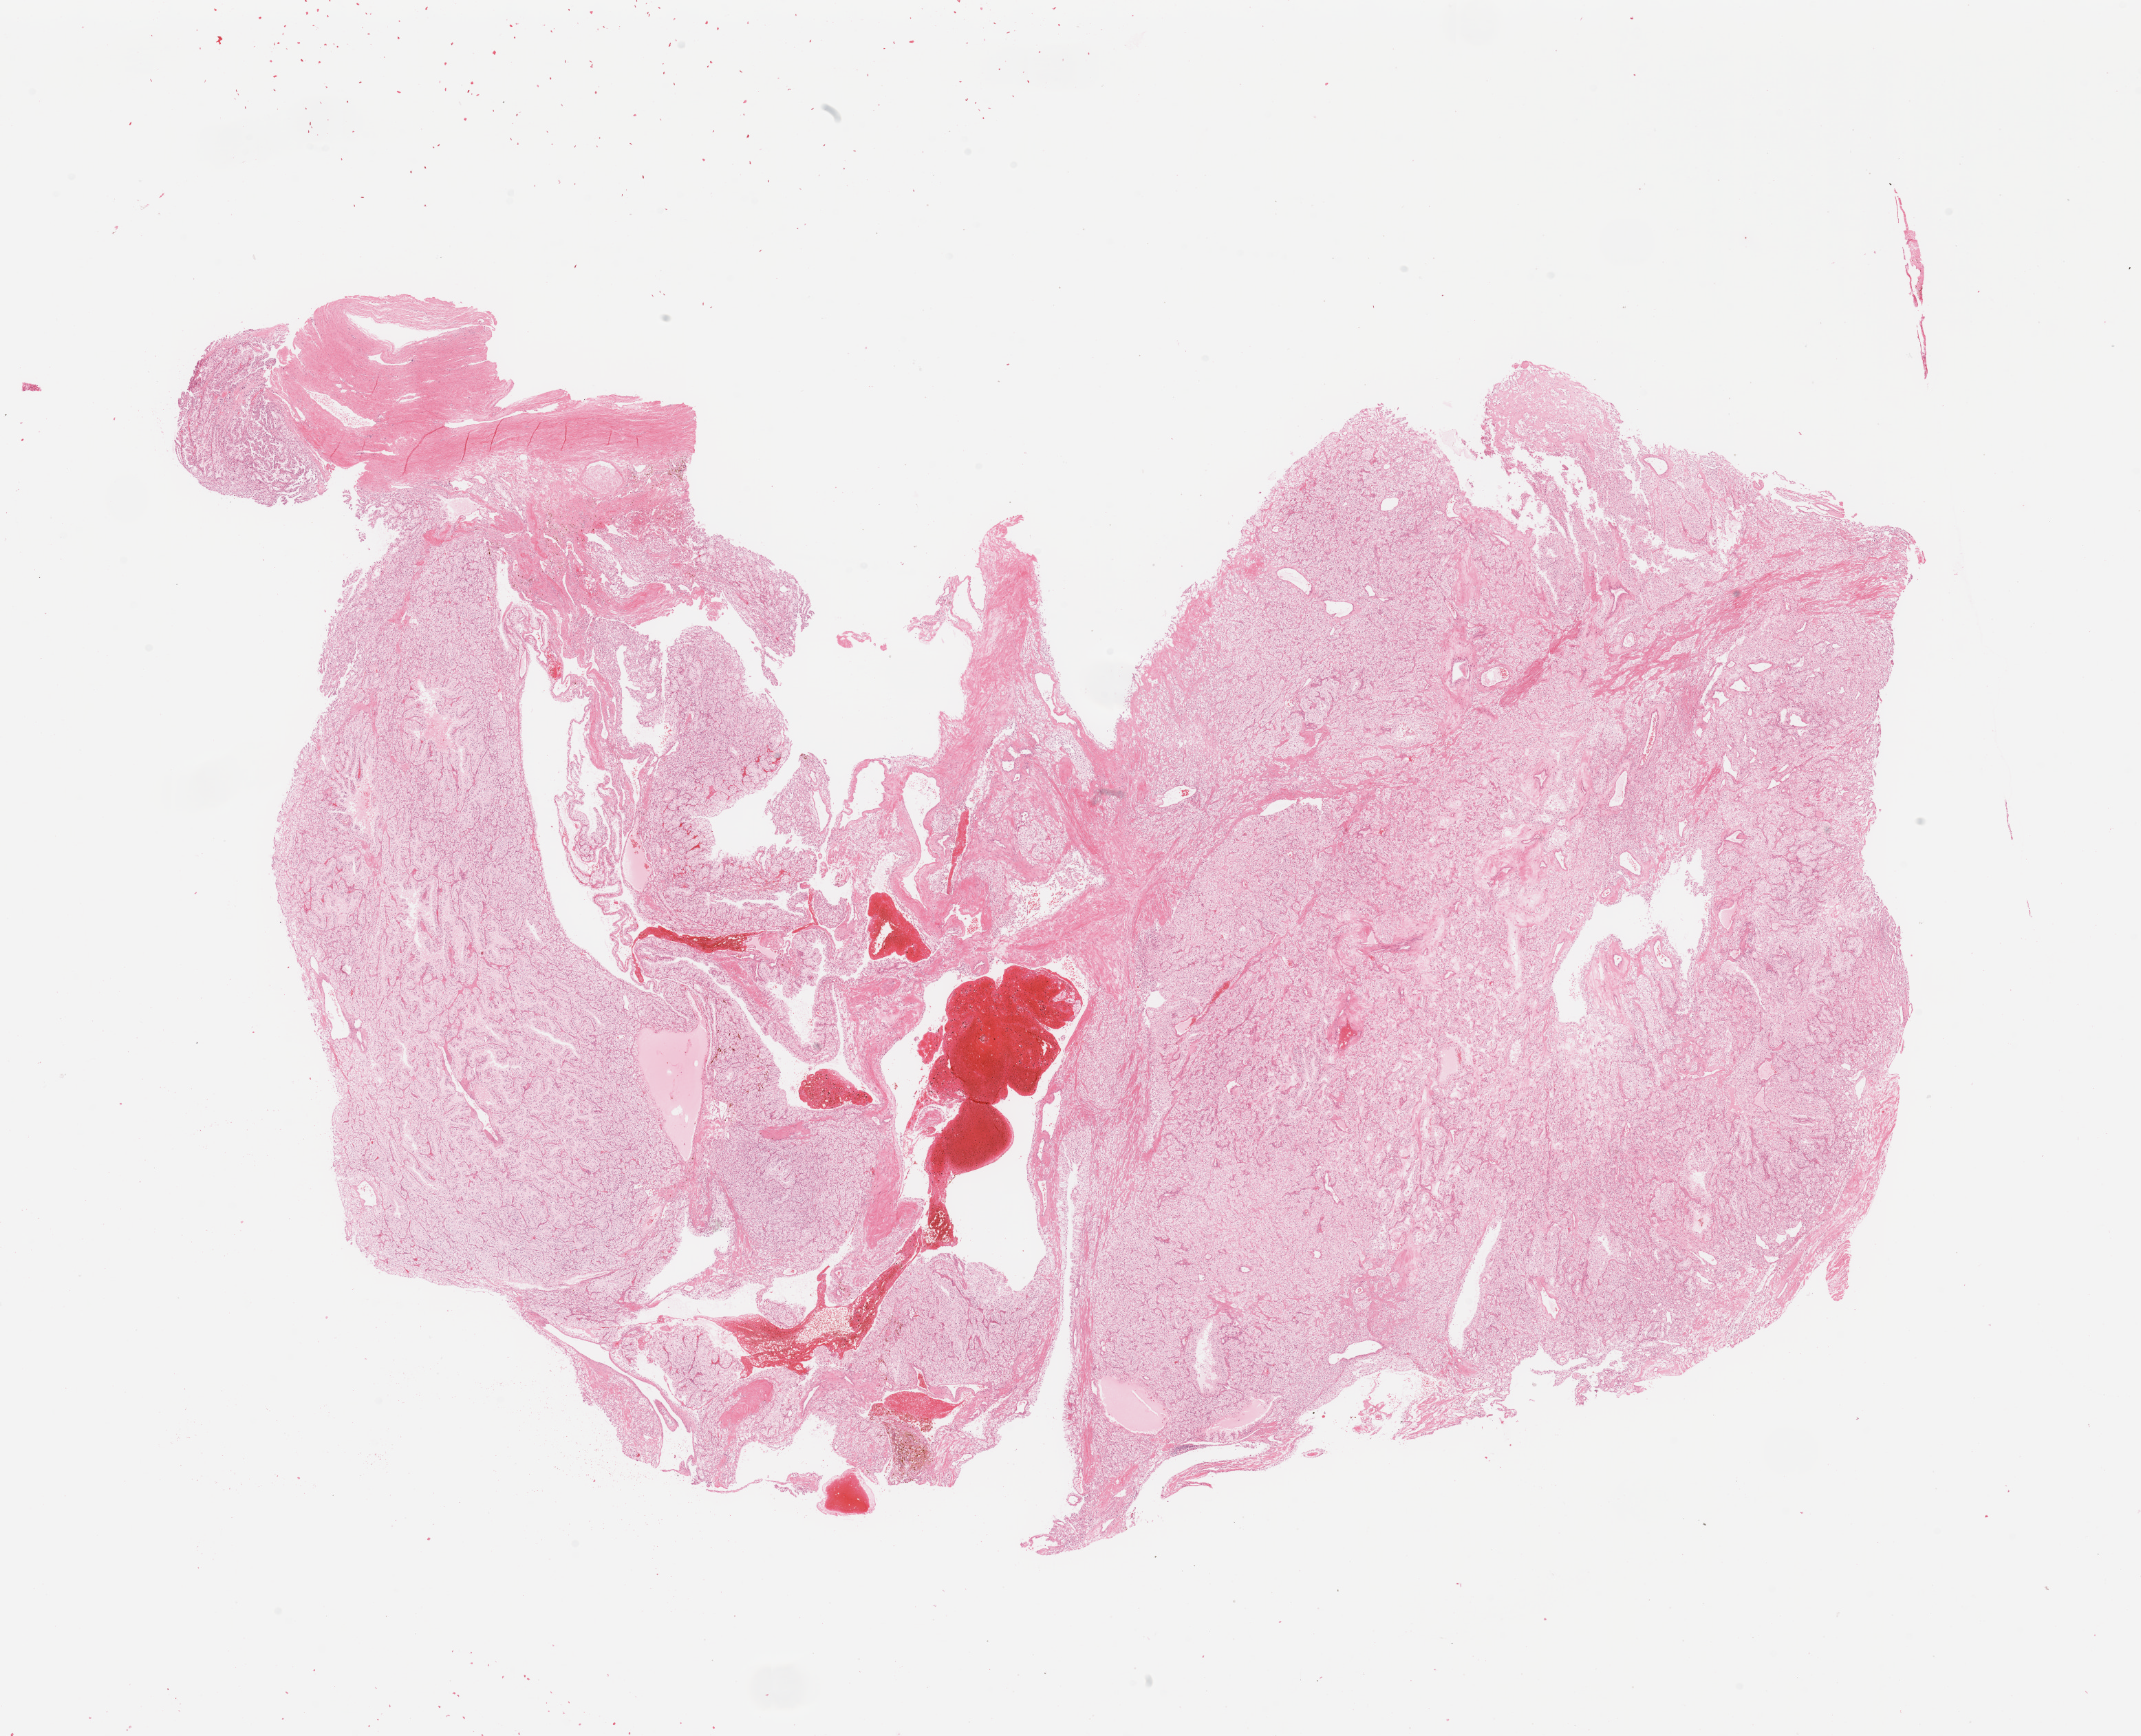
Whole-slide histology image, H&E-stained, whole scanned area (about 24.6 x 20.0 mm, acquisition: 20x scan) shown as a low-resolution overview; tumour tissue sample, sampled site: kidney. Male, 51 y/o. Histologic grade: G2 (moderately differentiated). Pathologist review of this section (percent, as recorded): tumour nuclei 80%, necrosis 3%.
* histologic diagnosis: Renal cell carcinoma, NOS